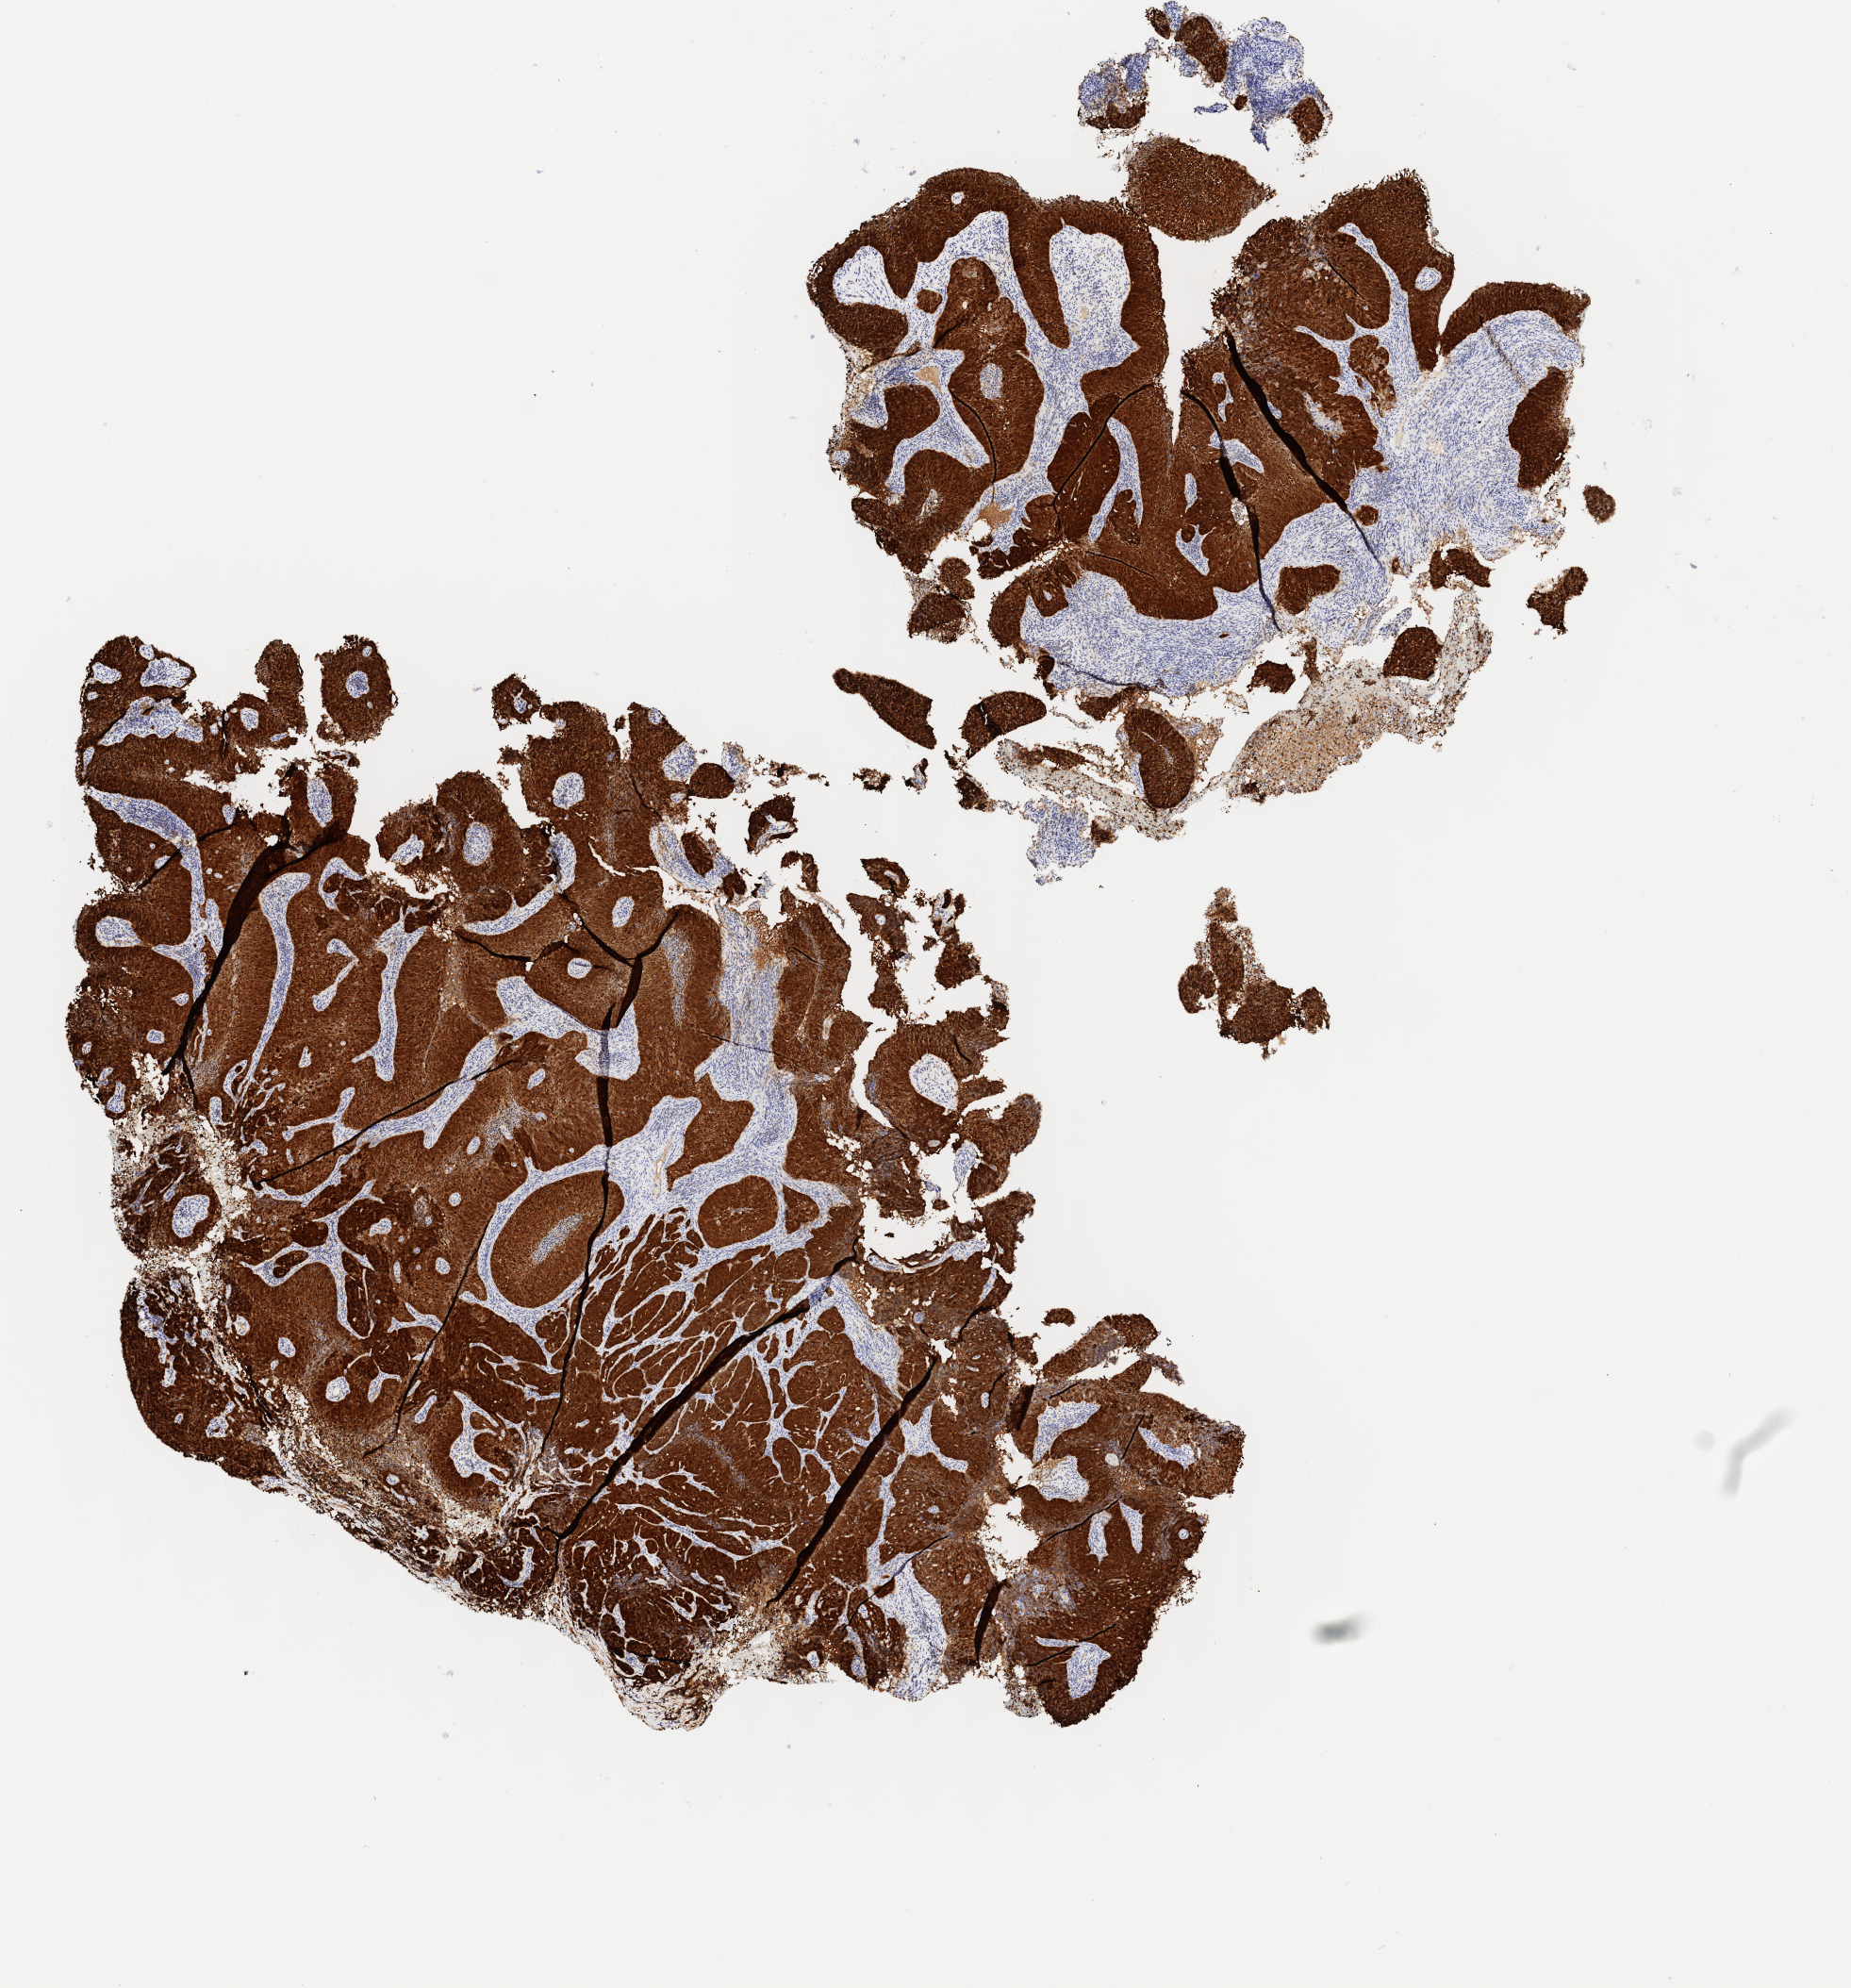
Immunohistochemistry (IHC) whole-slide image stained for p16 (p16INK4a), shown as a low-resolution overview of the whole scanned area (about 7.8 x 8.4 mm); tumor tissue; site: cervix. Patient female; age 38 years.
Diagnosis: Squamous cell carcinoma, large cell, nonkeratinizing, NOS.